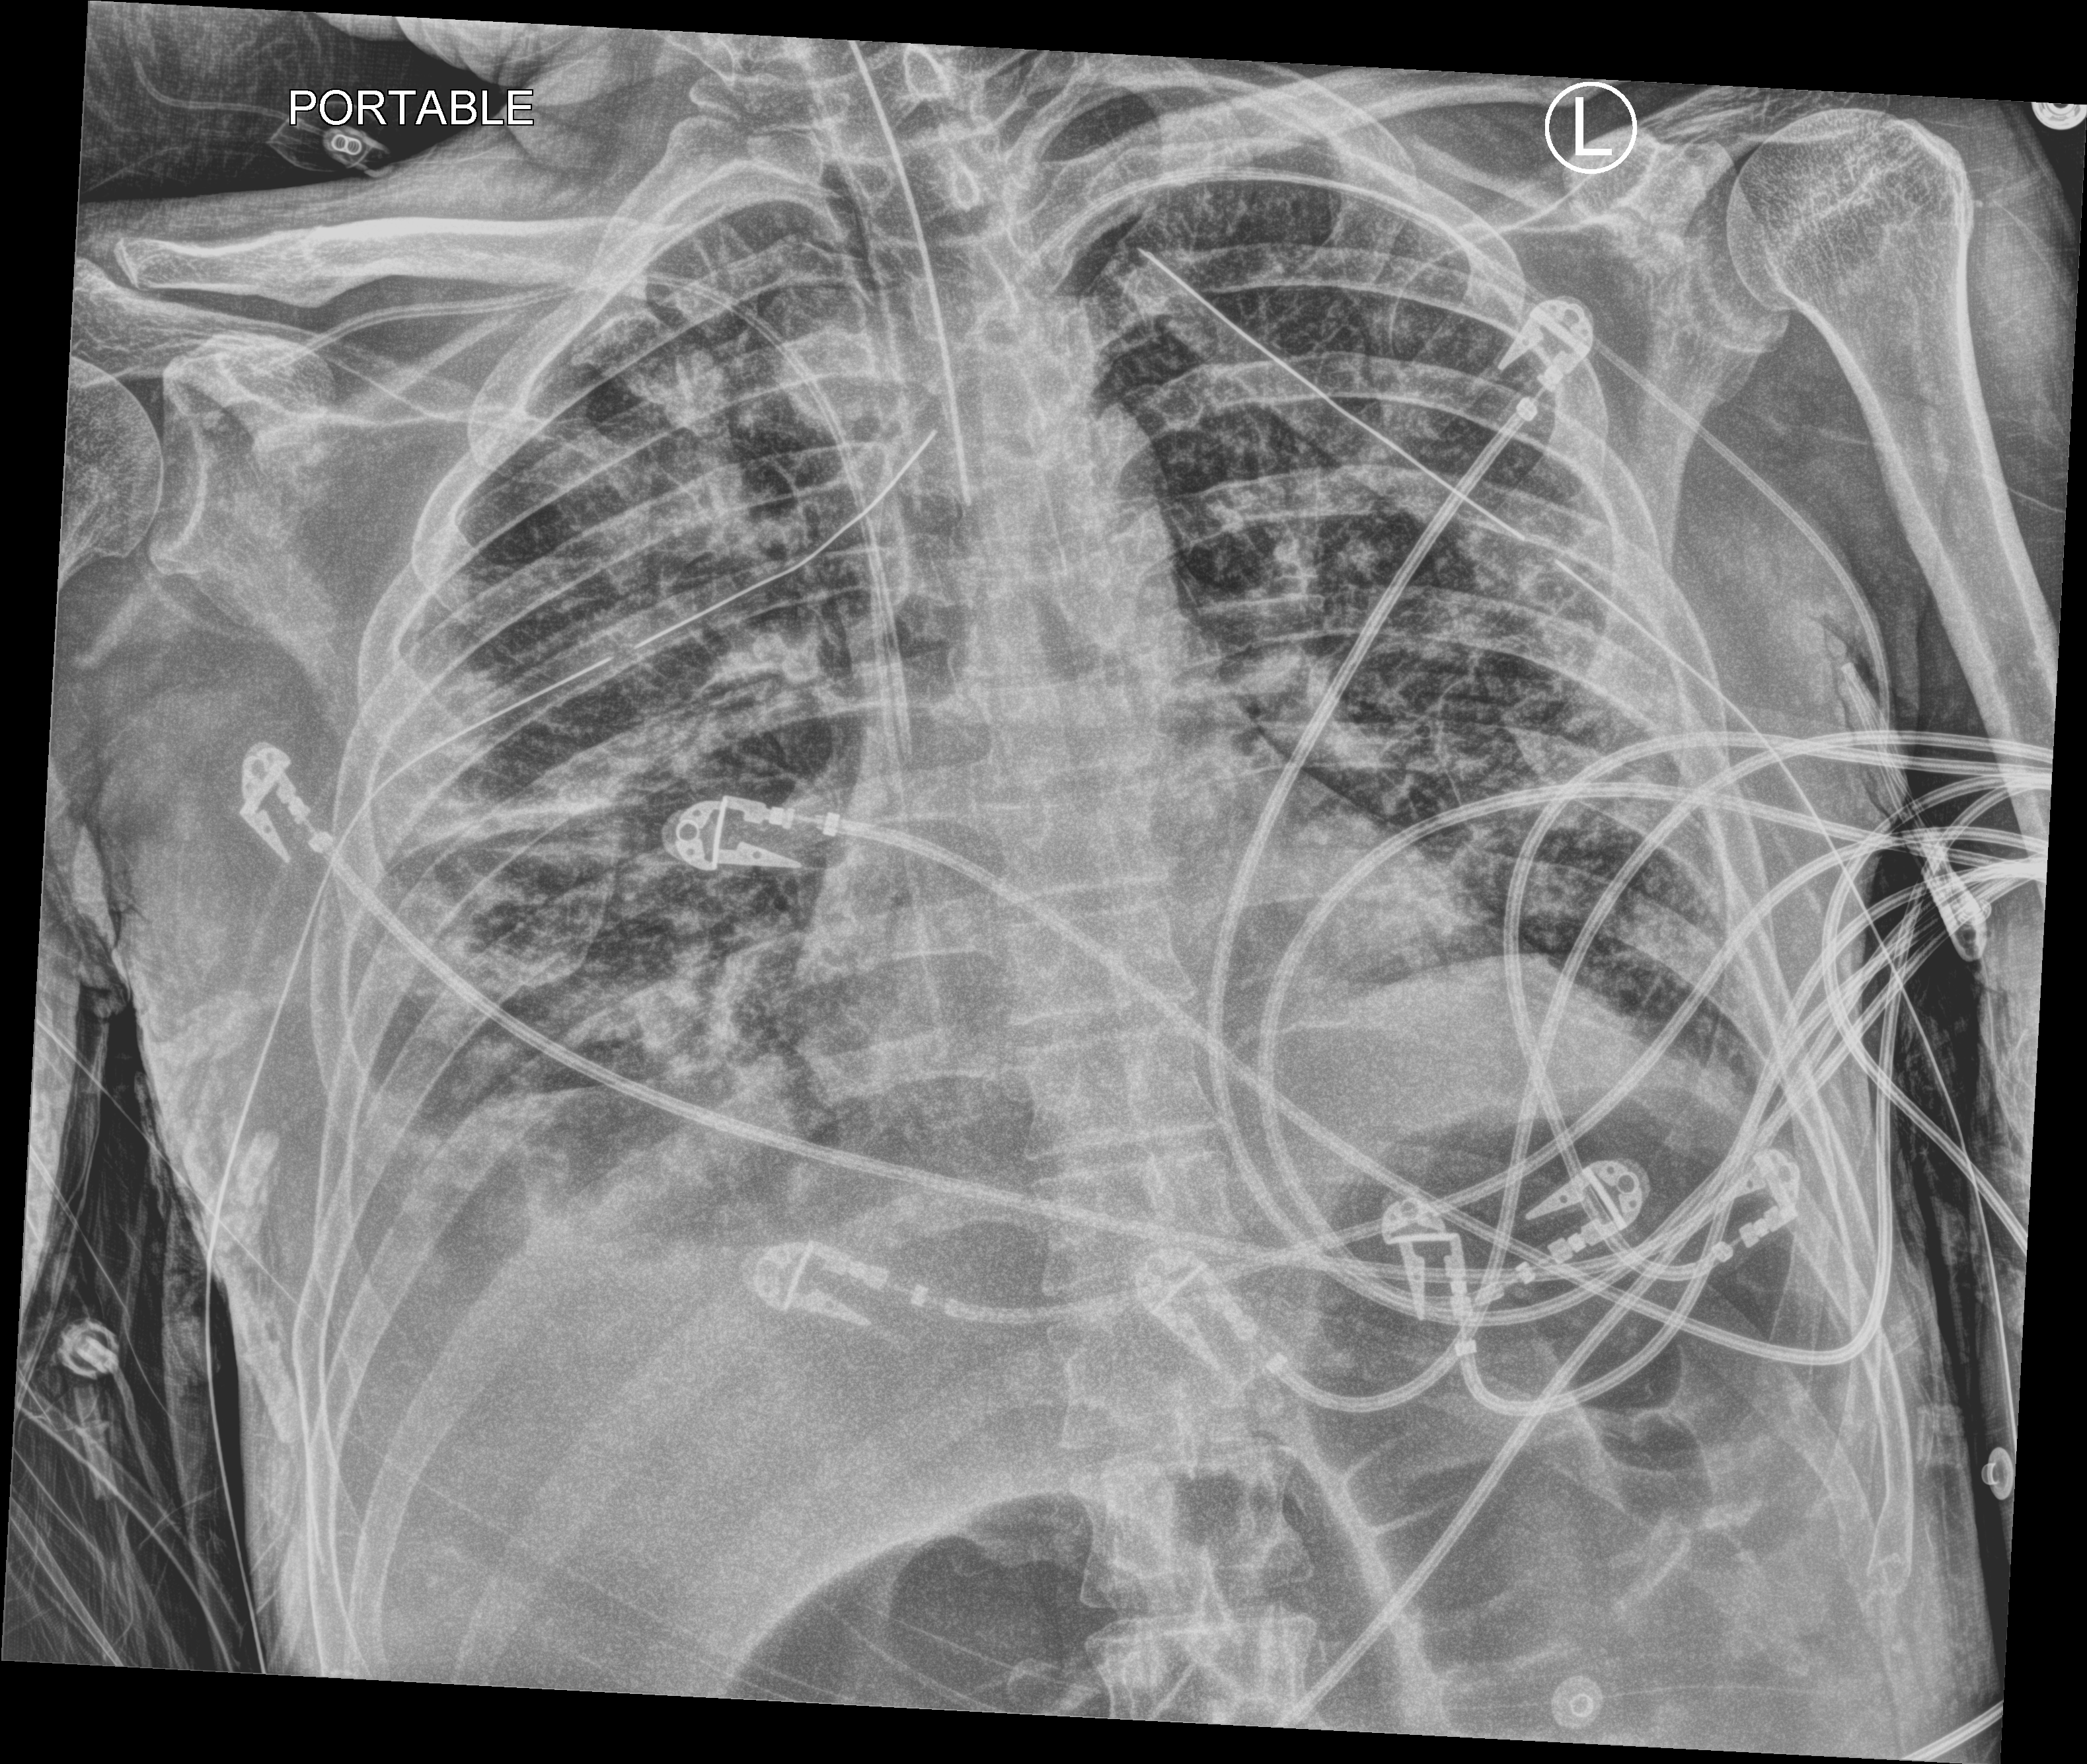
Bedside chest radiograph (computed radiography); anteroposterior (AP) projection. Male patient hospitalised with COVID-19, age 18–59 years.
Hospital-stay facts (about this admission, not read from this image; timing relative to this image not recorded):
- admitted to intensive care during this hospital stay: yes